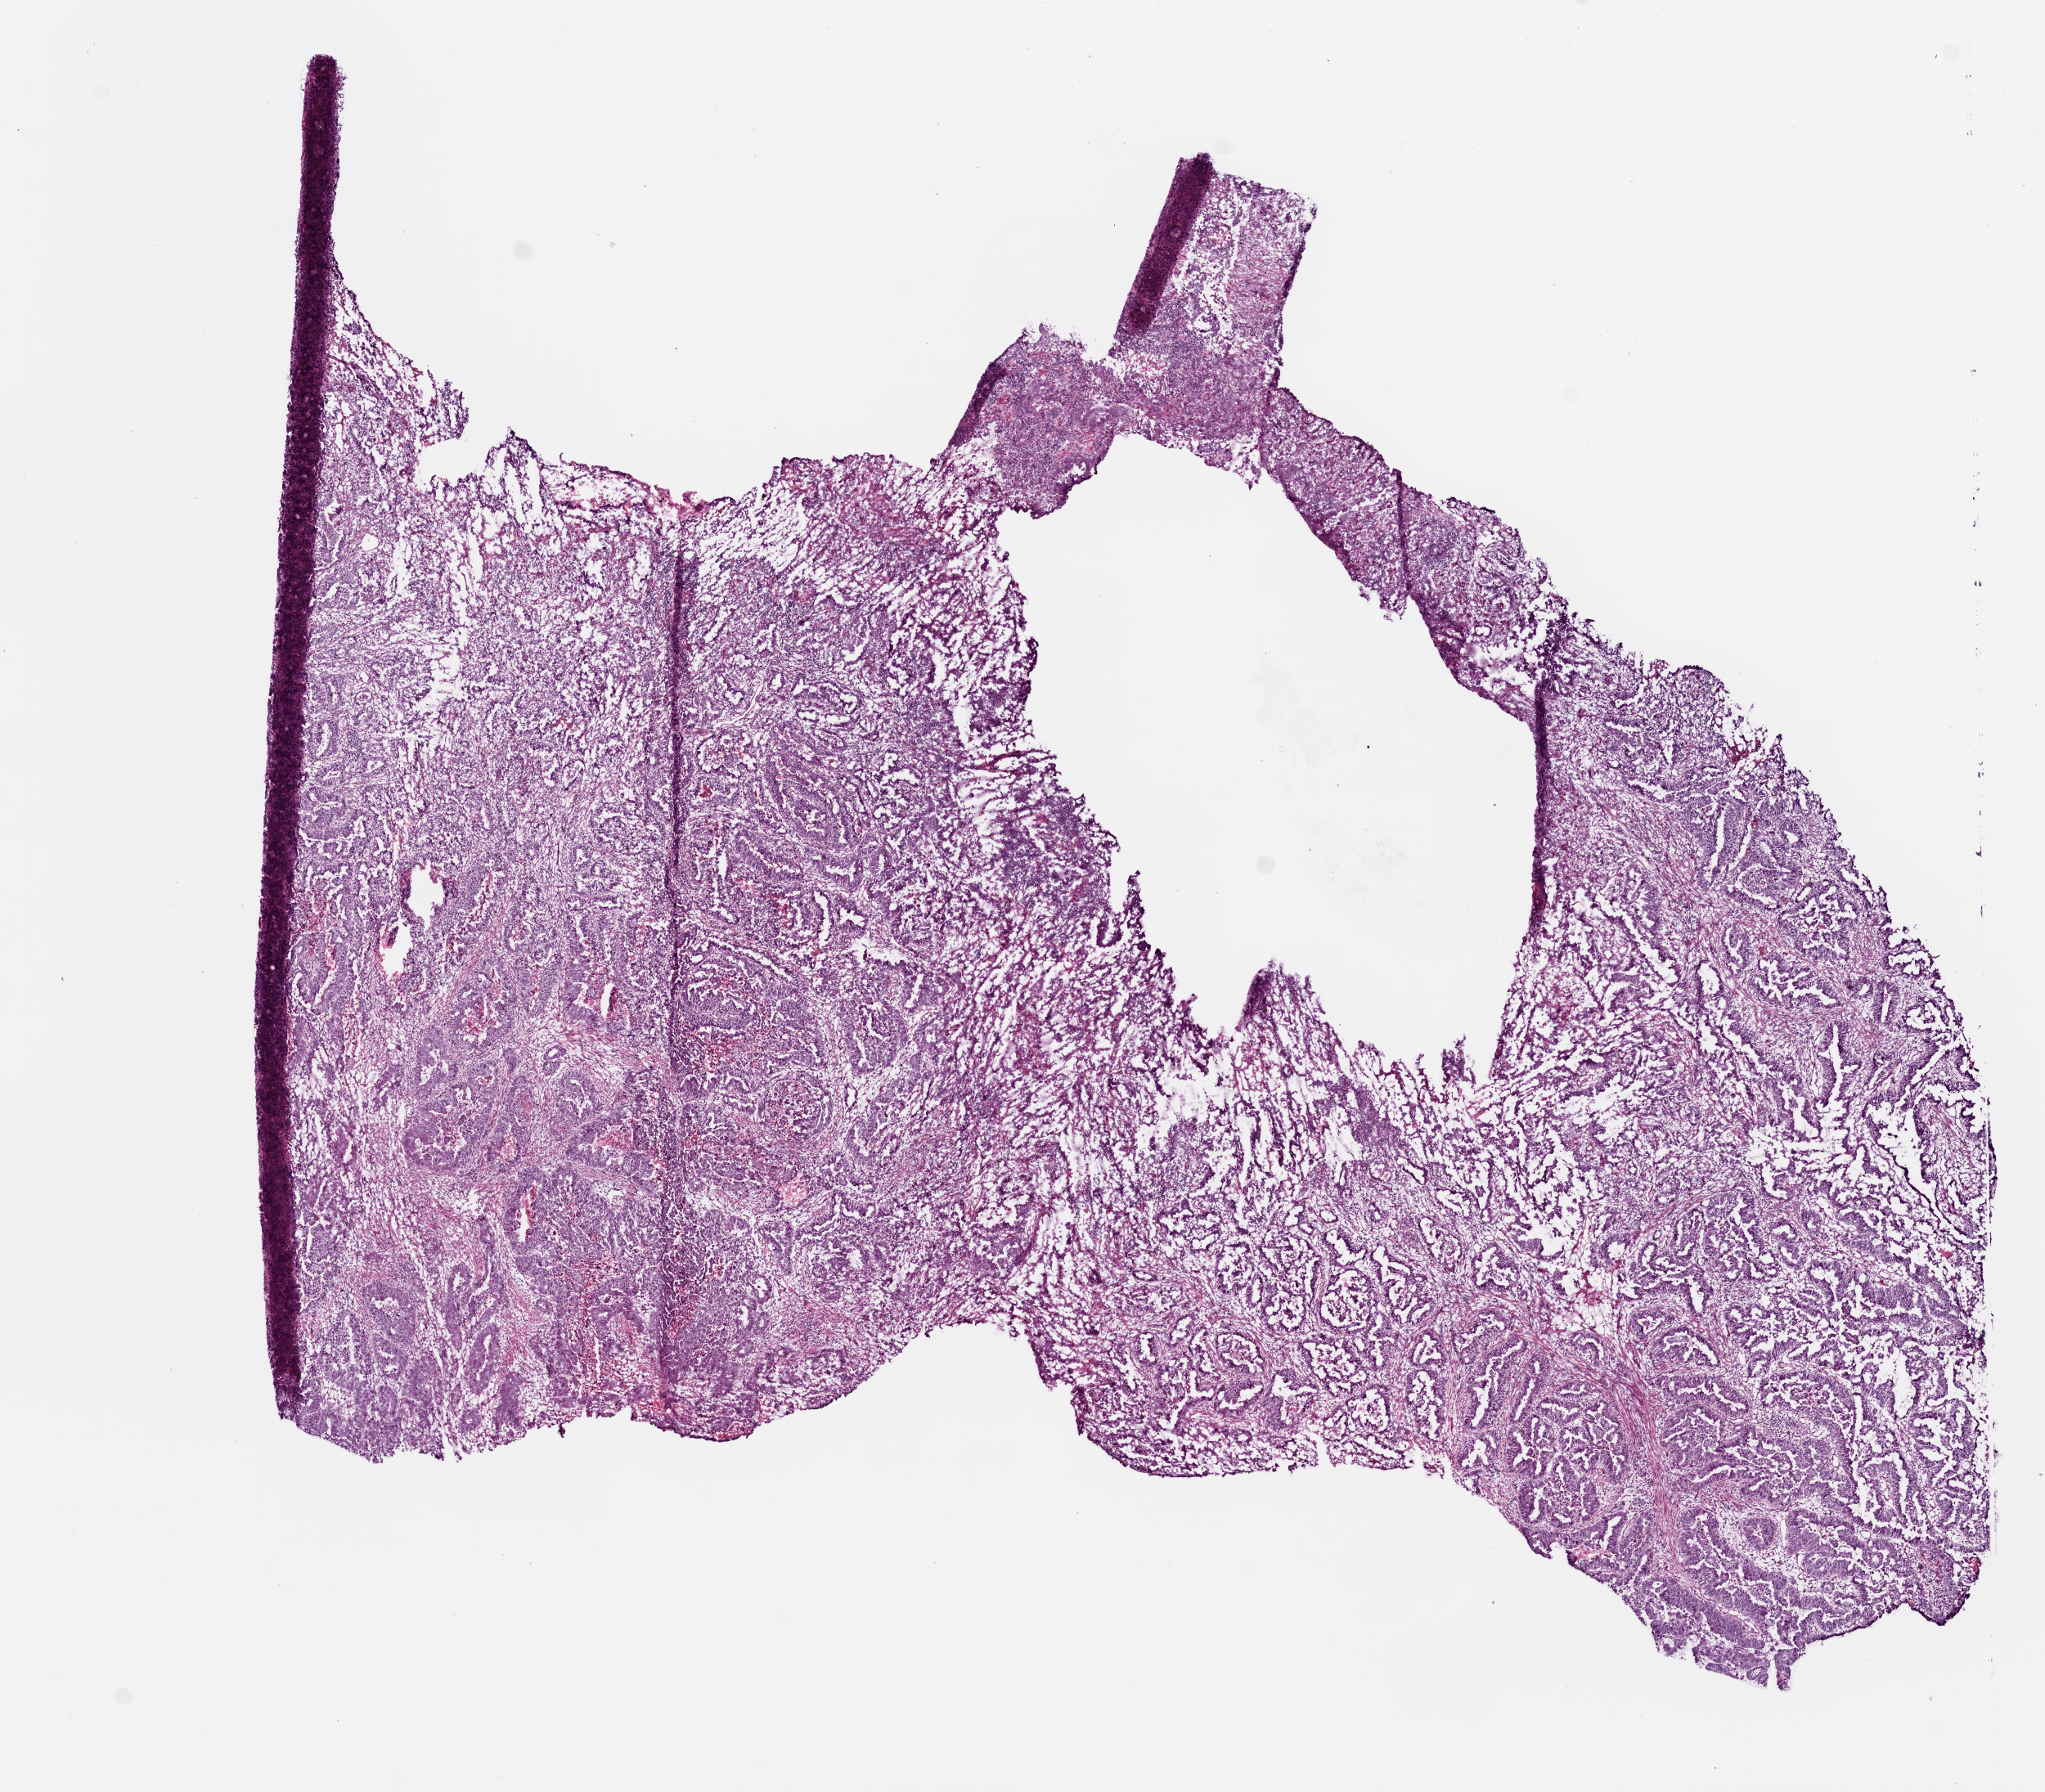
Hematoxylin and eosin (H&E) stained whole-slide image, whole scanned area (about 10.0 x 8.8 mm) shown as a low-resolution overview; frozen section from the bottom of the tissue portion; stomach, primary tumour sample. Female, age 80 years at initial diagnosis. Histologic grade: G2 (moderately differentiated). Composition of this section per pathologist review: tumour cells 73%, tumour nuclei 80%, normal cells 0%, stromal cells 15%, necrosis 12%.
AJCC pathologic stage: IV (5th edition). TNM: T2 N1 M1. Diagnosis: Adenocarcinoma, intestinal type.